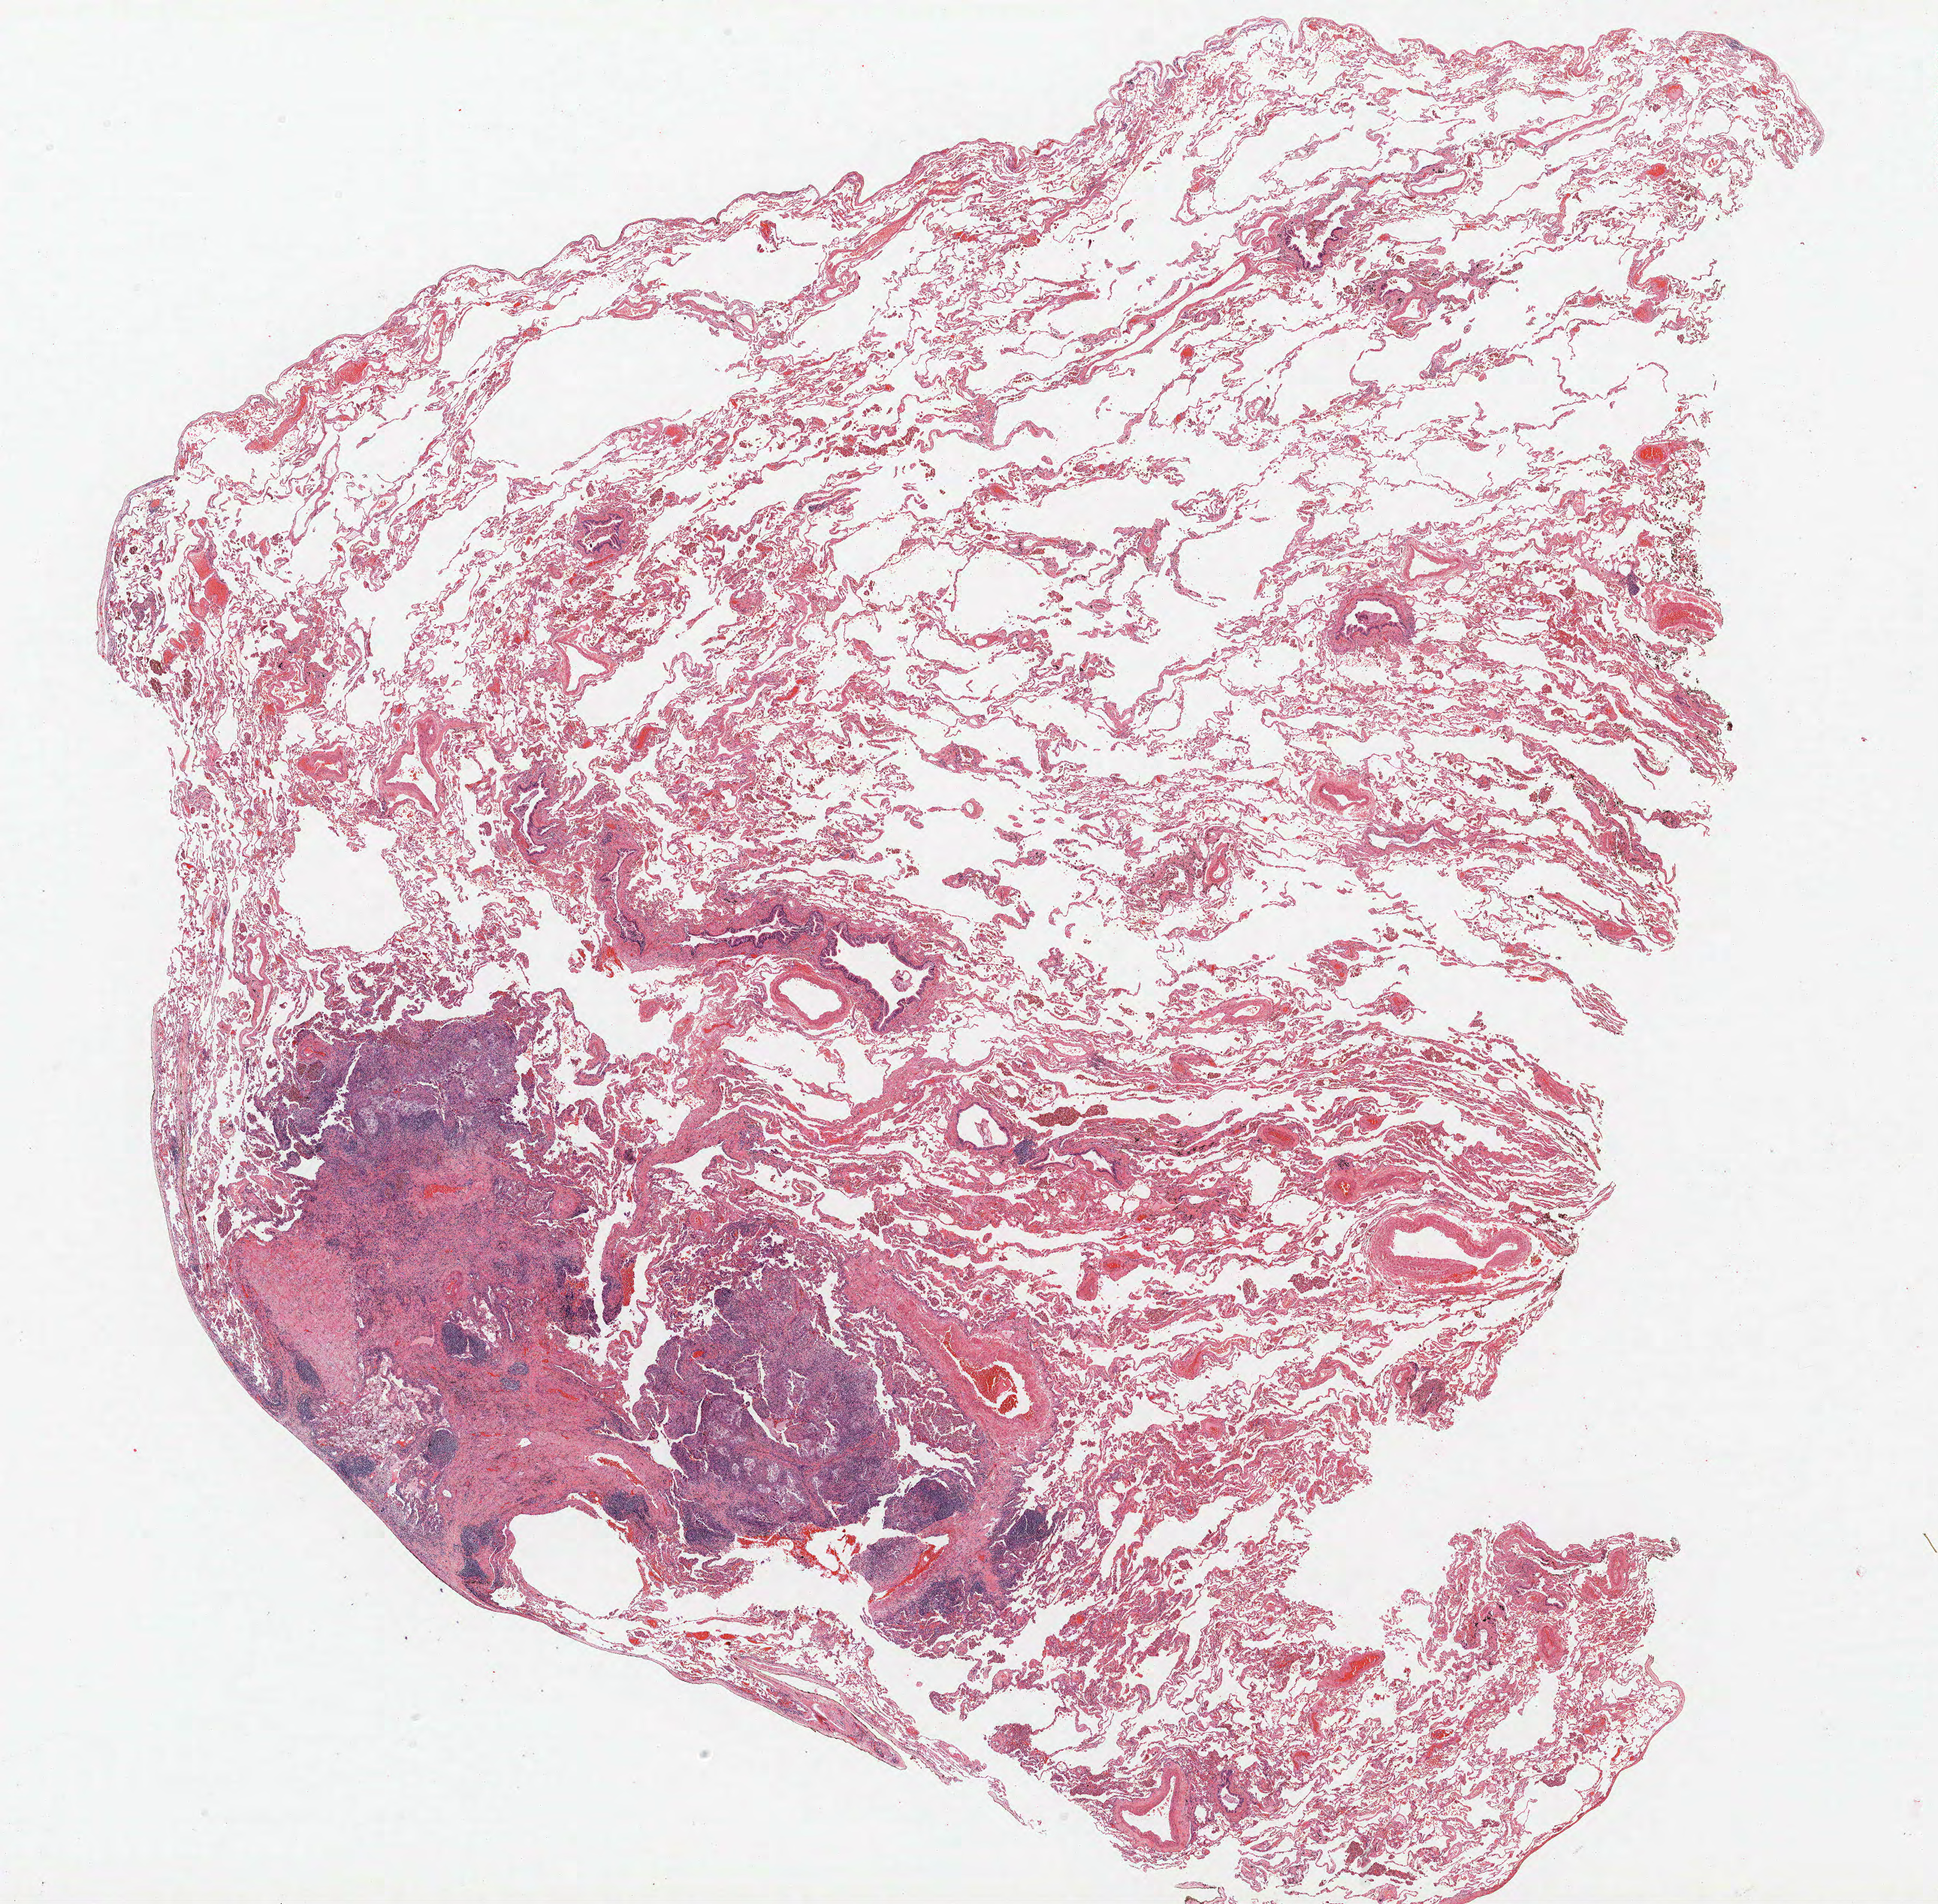
Whole-slide histology image, H&E, shown as a low-resolution overview of the whole scanned area (about 20.6 x 20.3 mm, from a 40x scan). FFPE section. Lung. Female, age 67 at enrolment. Current smoker at enrolment. Grade: poorly differentiated (G3).
• primary tumour location (clinical record): left upper lobe
• participant's lung-cancer diagnosis: Adenocarcinoma, NOS
• tumour size (pathology): 13 mm
• stage (AJCC 6th edition): IA